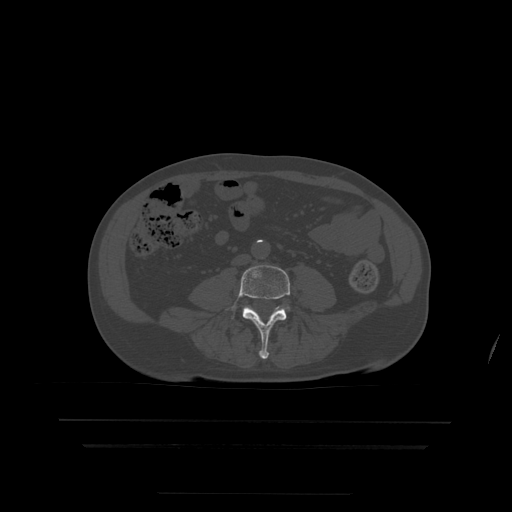
CT including the spine, one axial slice. Slice 93 of 522 in the series (ordered by position). Bone window (W 1800 / L 400 HU). 1.25 mm slice thickness. 512 × 512 image matrix, field of view 436 × 436 mm. Patient age 68 years. From the clinical record (not read from this slice): primary cancer: urothelial.
Outlined on this slice (semi-automatically segmented with operator editing):
- L4 vertebra: bounding box (x1, y1, x2, y2) in pixels: (227, 265, 291, 360)